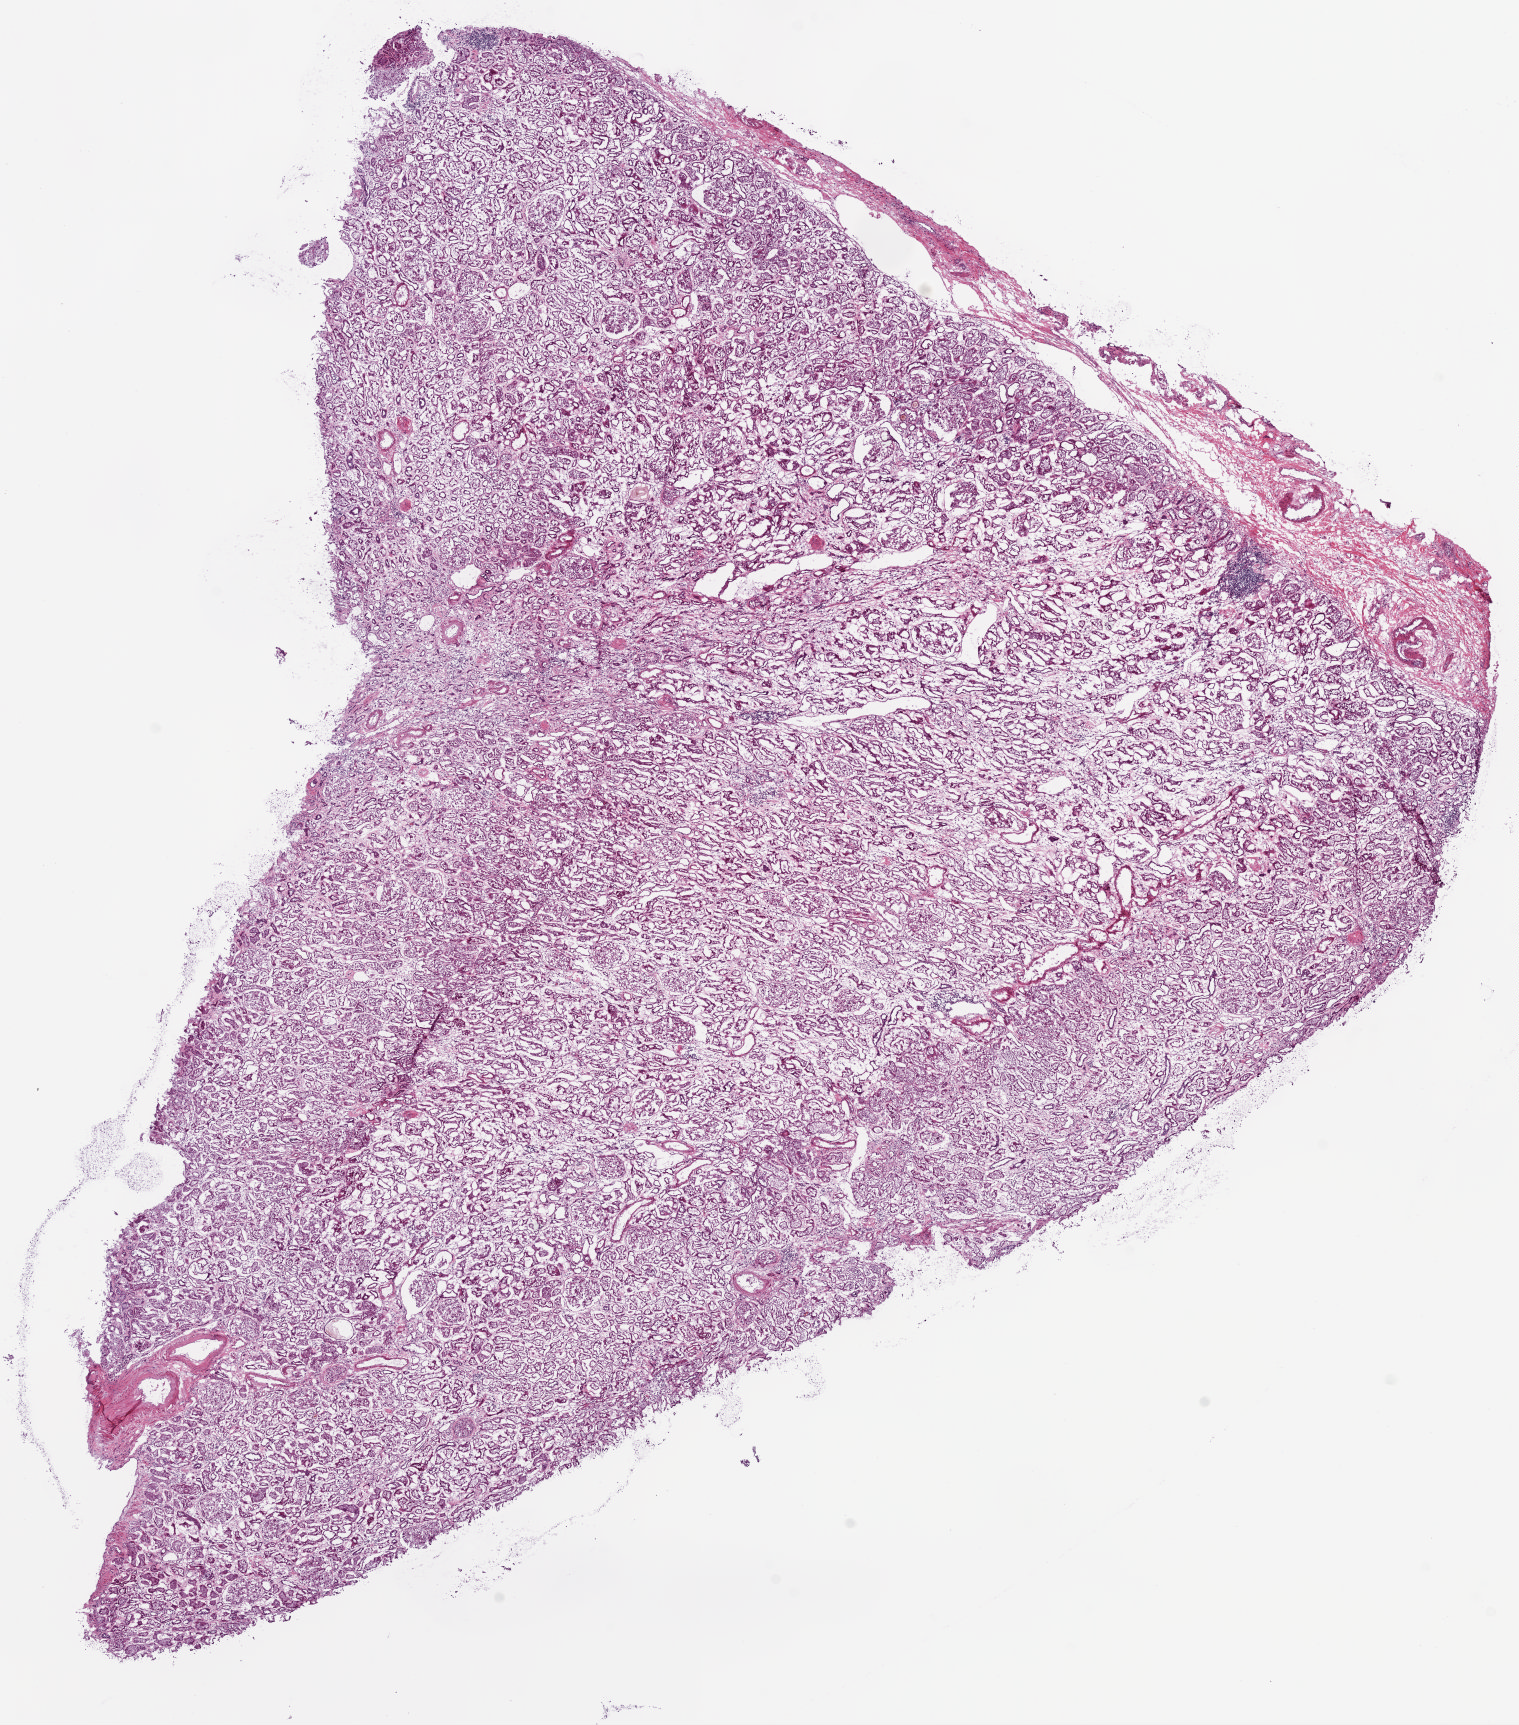
H&E-stained whole-slide image, shown as a low-resolution overview of the whole scanned area (about 12.2 x 13.8 mm). Frozen section from the top of the tissue portion. Solid tissue normal (non-tumour tissue) sample from the kidney. Male, age 64 years at initial diagnosis.
This section: solid tissue normal (non-tumour) sample from the same patient. Patient diagnosis: Clear cell adenocarcinoma, NOS.